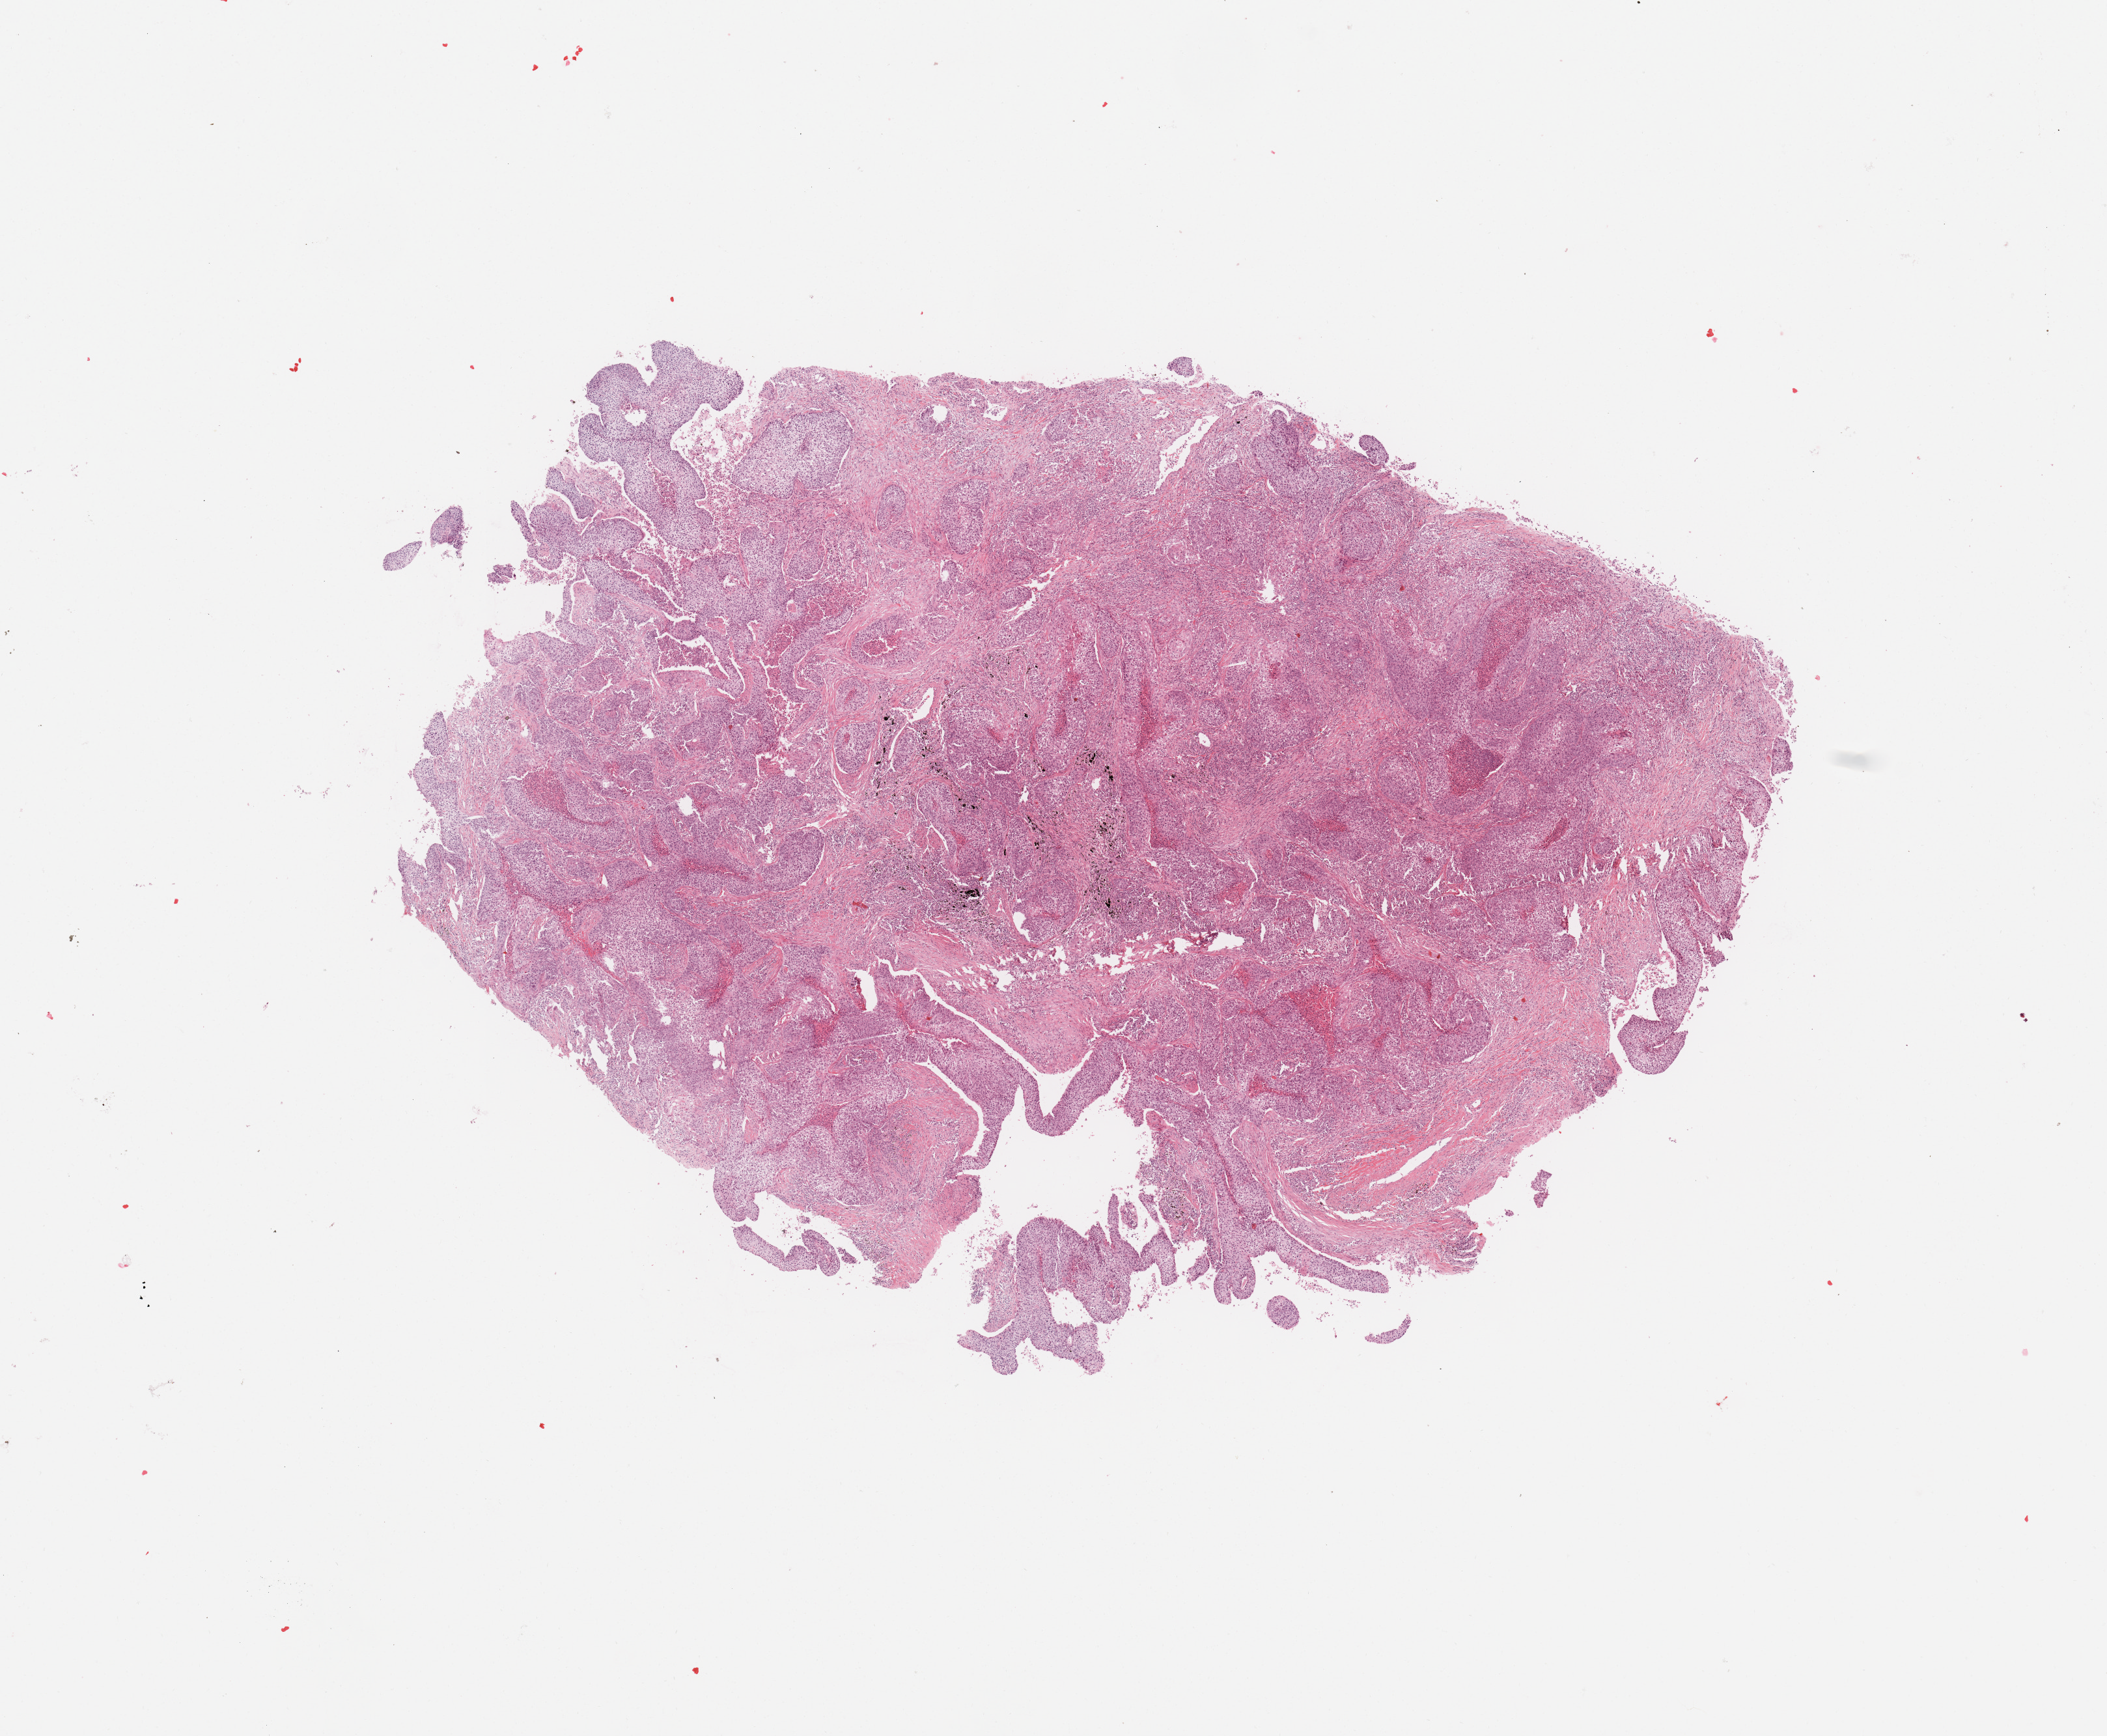
Whole-slide histology image, H&E-stained — a low-resolution overview of the entire scanned area, about 12.8 x 10.5 mm (from a 20x scan), tumour tissue sample, sampled site: lung. Patient: male, age 68 years. Histologic grade: G3 (poorly differentiated). Pathologist review of this section (percent, as recorded): tumour nuclei 85%, necrosis 5%.
* AJCC pathologic stage: IB
* histologic diagnosis: Squamous cell carcinoma, NOS
* primary tumour site (as recorded): right upper lobe